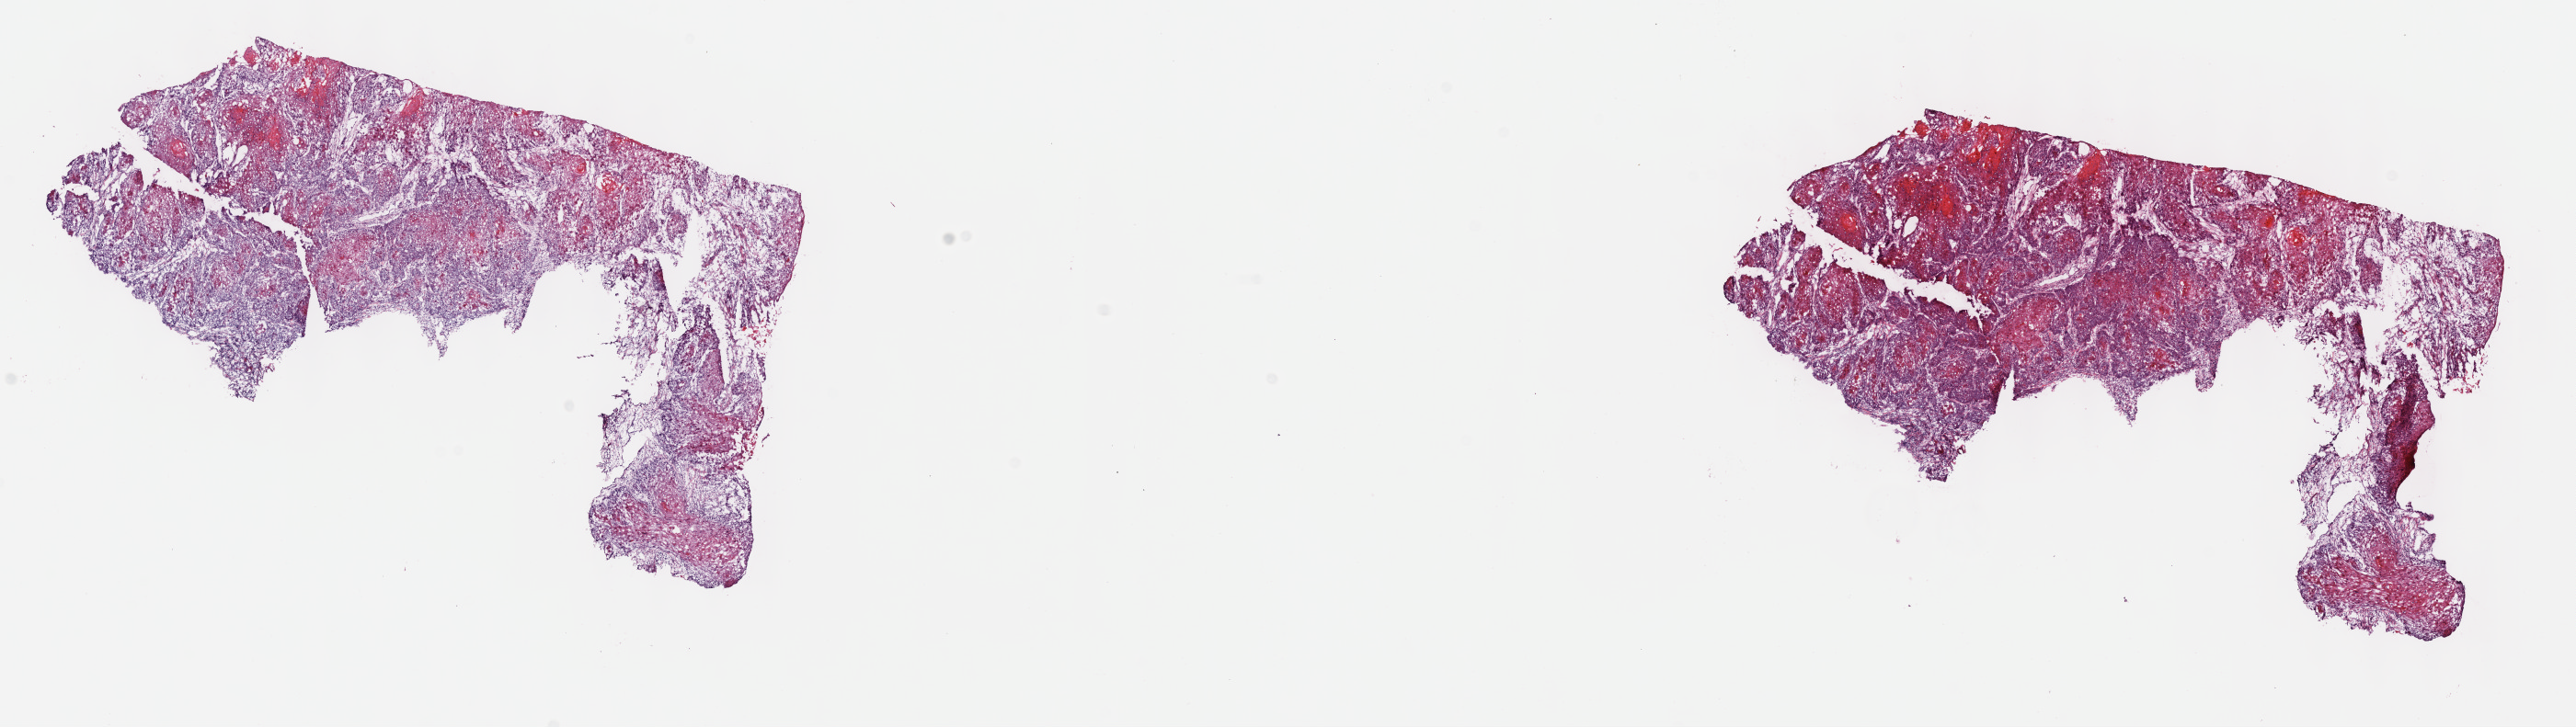
Whole-slide histology image, H&E — low-resolution overview of the scanned area, about 22.7 x 6.4 mm (acquisition: 40x scan), frozen section from the top of the tissue portion, primary tumour sample from the head and neck. Male patient; age at initial diagnosis 42 years. Histologic grade: G1 (well differentiated). Pathologist review of this section (percent, as recorded): tumour cells 60%, tumour nuclei 70%, normal cells 0%, stromal cells 40%, necrosis 0%. Inflammatory infiltration, as recorded: lymphocyte infiltration 0%, monocyte infiltration 0%, neutrophil infiltration 0%.
AJCC pathologic stage: IVA (7th edition). Laterality: left. Diagnosis: Squamous cell carcinoma, NOS.